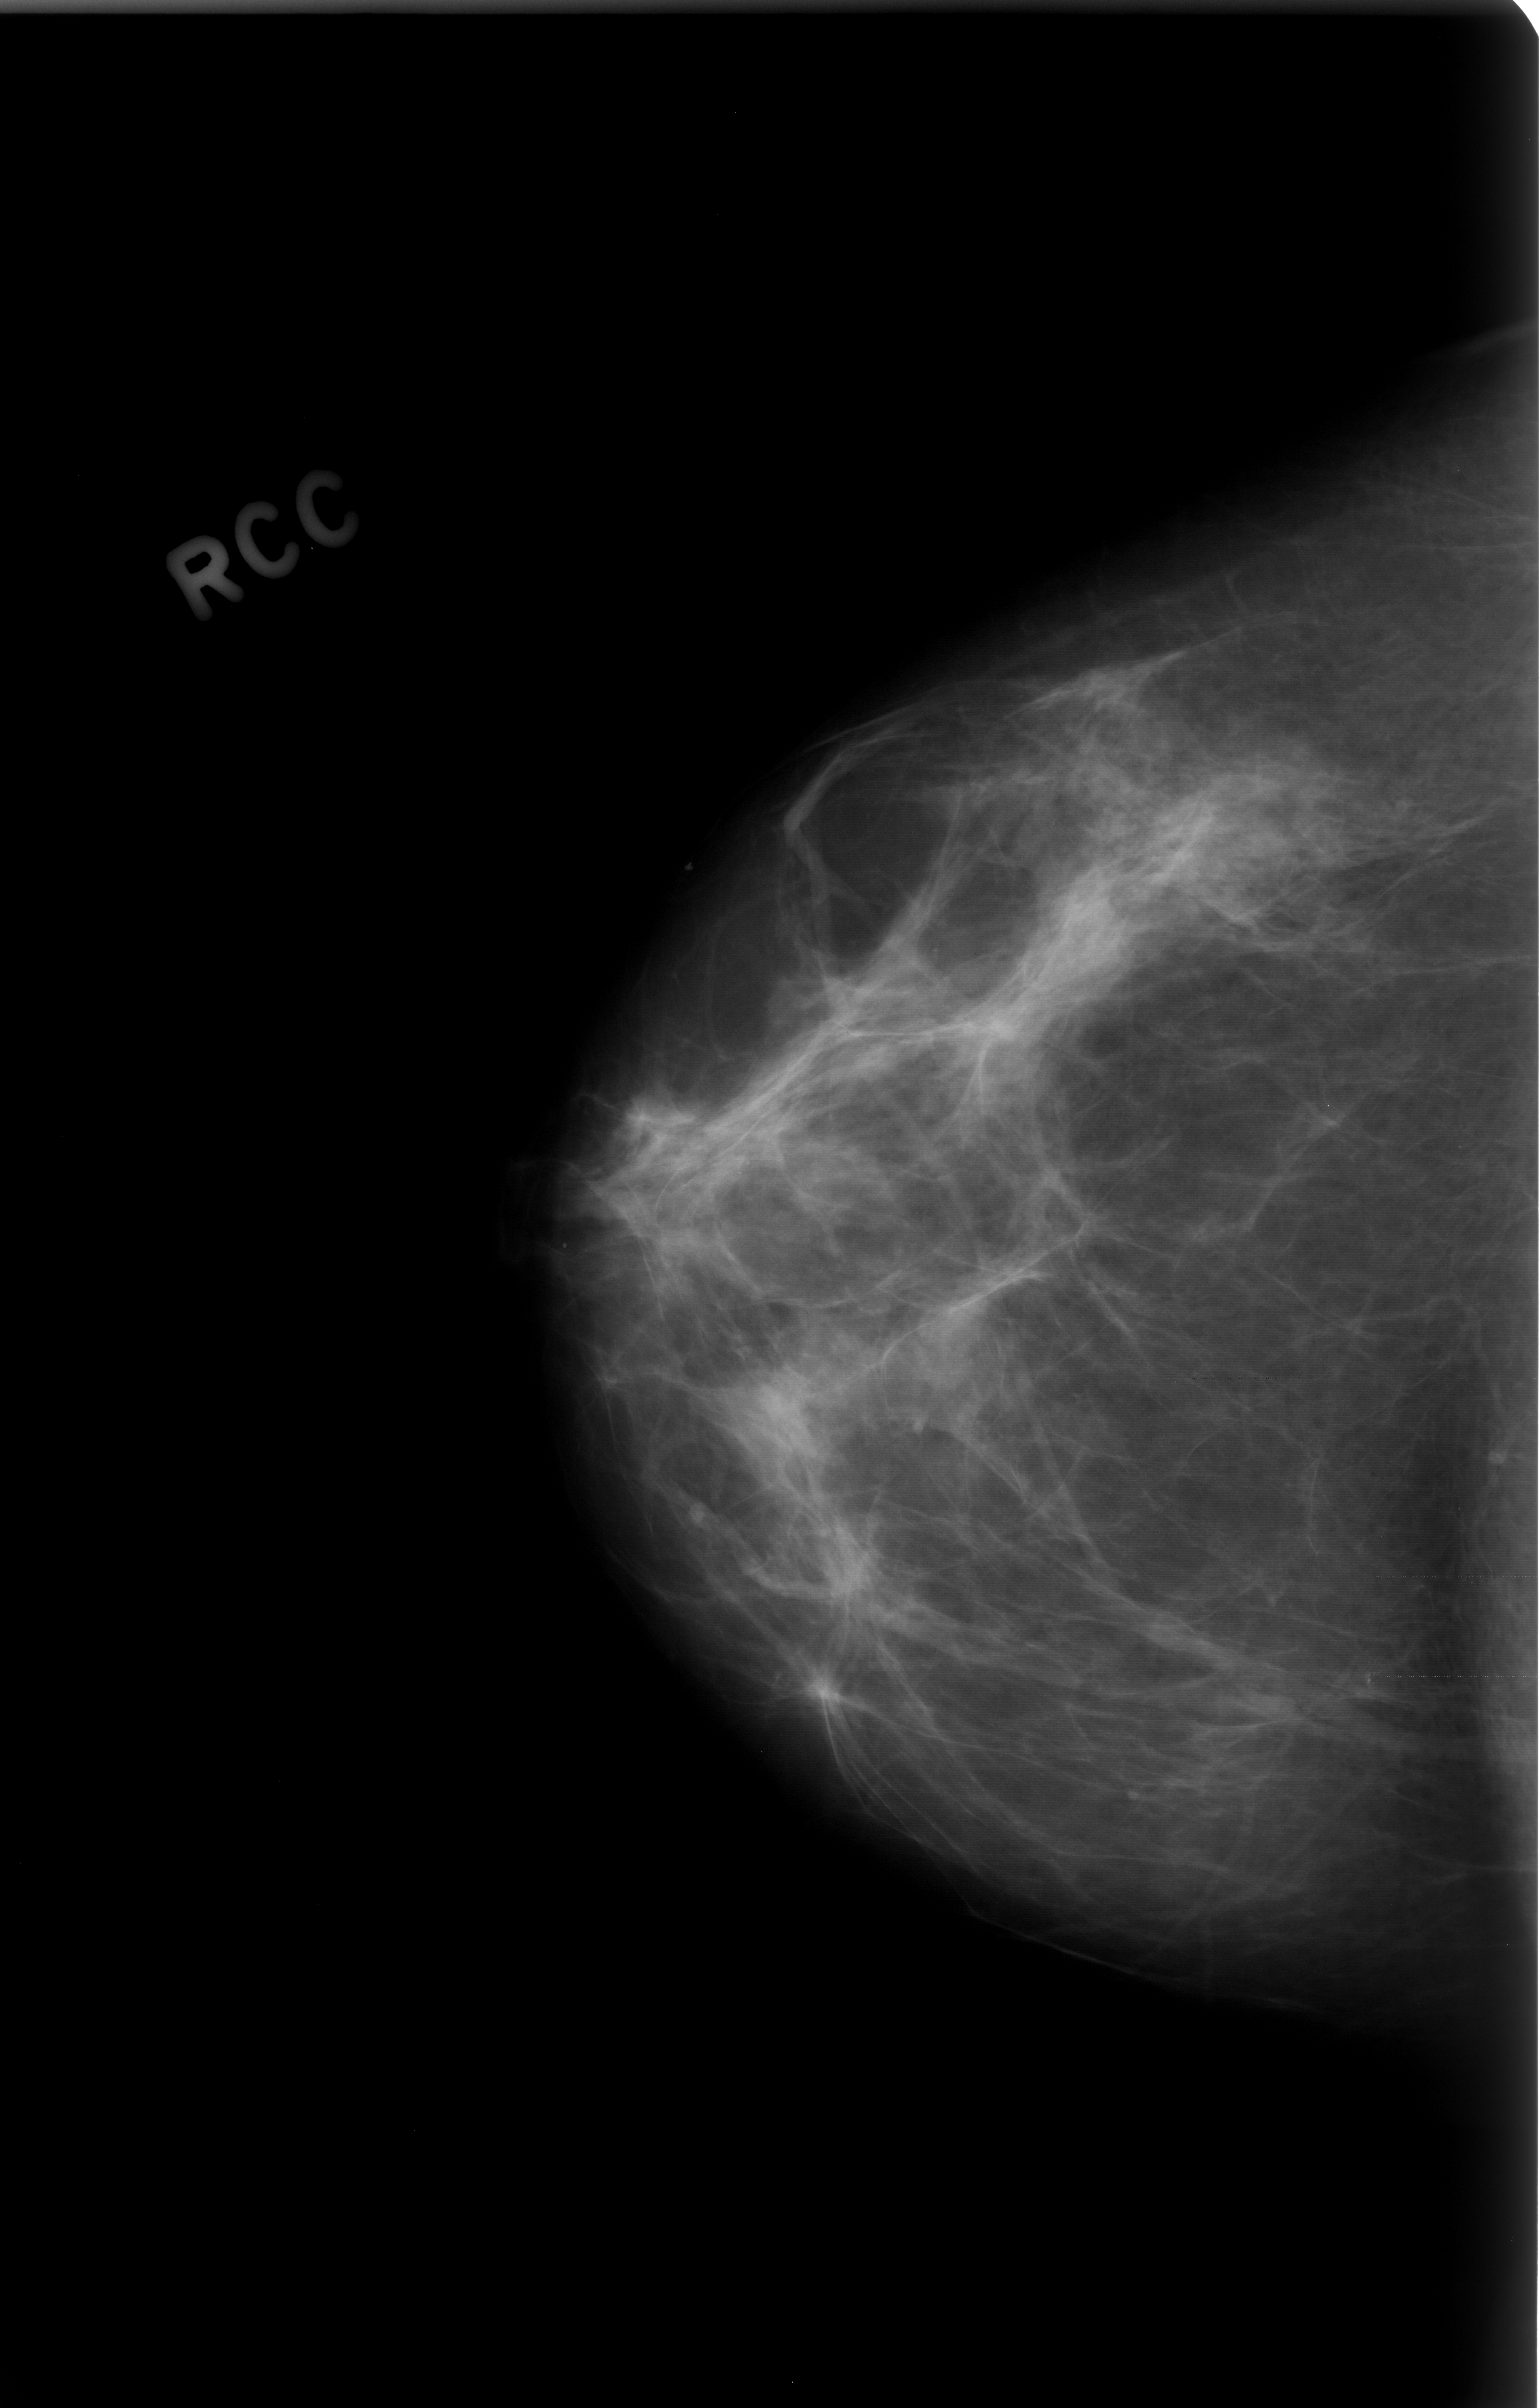
Scanned film-screen mammogram; right breast; craniocaudal (CC) view; breast composition: scattered fibroglandular densities (BI-RADS density category 2 of 4); 1539 × 2408 image matrix.
Expert-marked regions of interest on this image (one box per marked abnormality):
- calcifications, morphology amorphous, distribution clustered; BI-RADS assessment category 4; pathology (as recorded): benign: bounding box <1252,1611,1413,1786> (left, top, right, bottom; pixels)